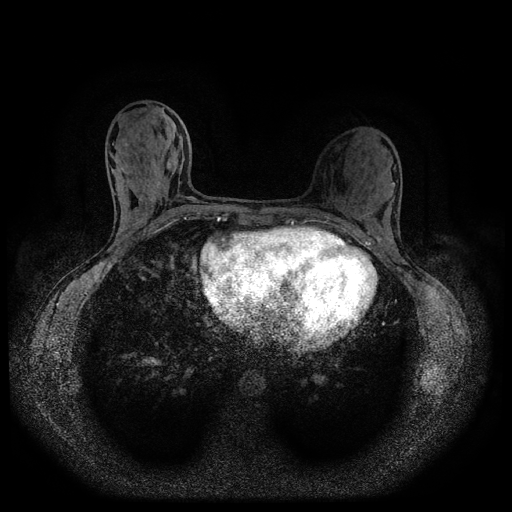
Breast MRI (dynamic contrast-enhanced, multi-phase), one axial slice; slice 43 of 116 in the series (ordered by position); dynamic contrast-enhanced series, time point 2 of 5 at this slice position (early post-contrast); 1.5 T; TE 2.7 ms, TR 5.4 ms; 2 mm slice thickness; 512 × 512 image matrix. Female patient, age 32 years.
Annotated regions visible in this slice (semi-automatic segmentation, software-assisted and operator-edited):
- breast lesion (labelled benign in the annotation): bounding box [x1, y1, x2, y2] px = [164, 156, 172, 173]